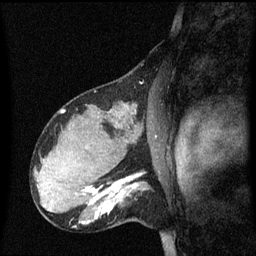
Breast MRI (dynamic contrast-enhanced), one sagittal slice; position 39 of 60 along the scan axis; dynamic contrast-enhanced series, image 2 of 3 at this slice position (ordered by acquisition); 1.5 T; TE 4.2 ms, TR 8.4 ms; 2.1 mm slice thickness; 256 × 256 image matrix, field of view 210 × 210 mm. Patient: female, 31 years. Case-level facts recorded for this patient, not image findings: setting: breast cancer imaged before/during neoadjuvant chemotherapy; receptor status: HR-positive, HER2-negative.
Annotated regions visible in this slice (semi-automatic segmentation, software-assisted and operator-edited):
- analysis volume of interest (the breast-tissue region the enhancement analysis was run in; not a lesion): bounding box <98,175,150,227> (left, top, right, bottom; pixels)
- tumour enhancement mask (voxels above the 70 % enhancement threshold inside the analysis volume of interest): <98,175,140,218>